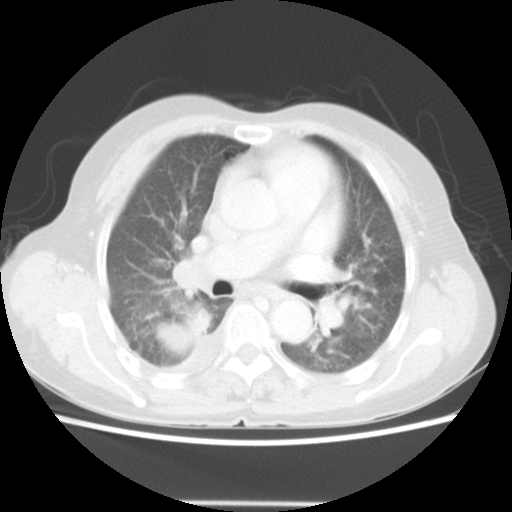
Chest CT, one axial slice. Slice 30 of 52 in the series (ordered by position). 140 kVp. Lung window (W 1500 / L -600 HU). 512 × 512 image matrix, field of view 337 × 337 mm. Female patient, age 67 years. Case-level facts recorded for this patient, not image findings: clinical TNM (as recorded): T3 N1 M1.
Annotated regions visible in this slice (bounding box drawn by a radiologist):
- lung tumour (recorded histology: adenocarcinoma): bounding box [x1, y1, x2, y2] px = [152, 298, 212, 356]